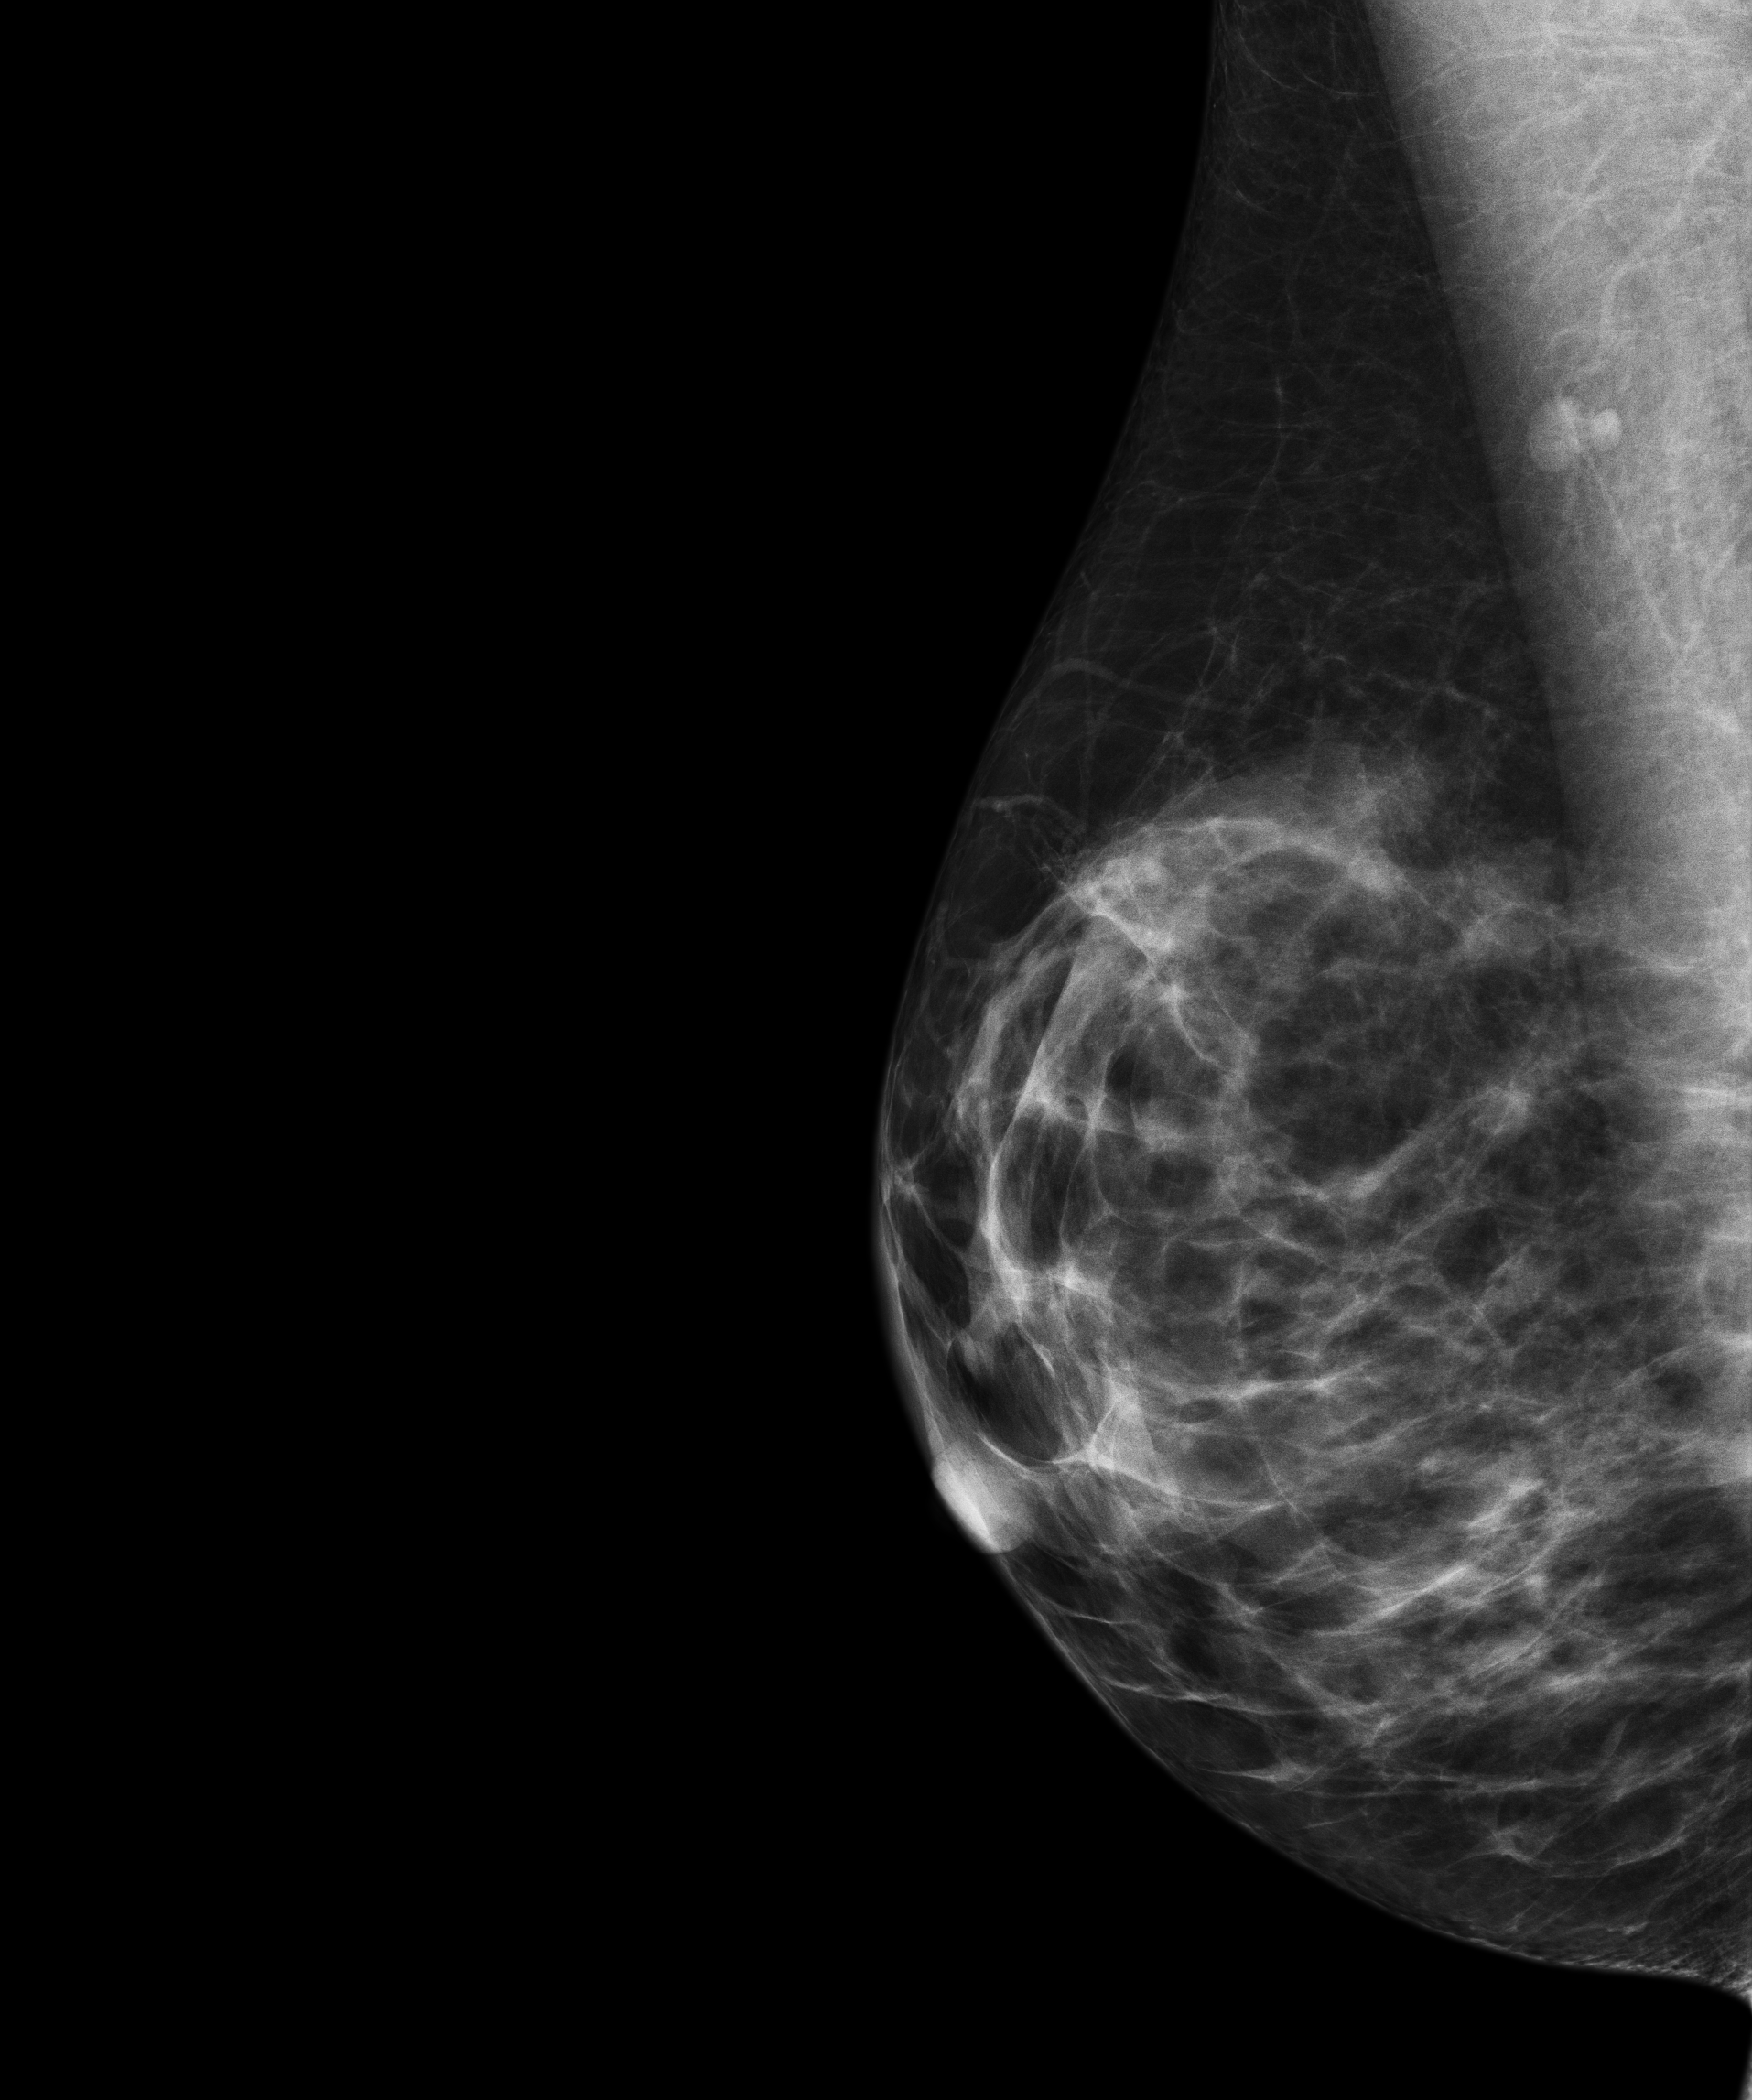
Digital mammogram (FFDM), right breast, medio-lateral oblique projection, annual screening mammography examination, compressed breast thickness 47 mm. Female patient, age 45 years.
Final BI-RADS assessment for this screening round (tomosynthesis exam, both breasts): category 1.